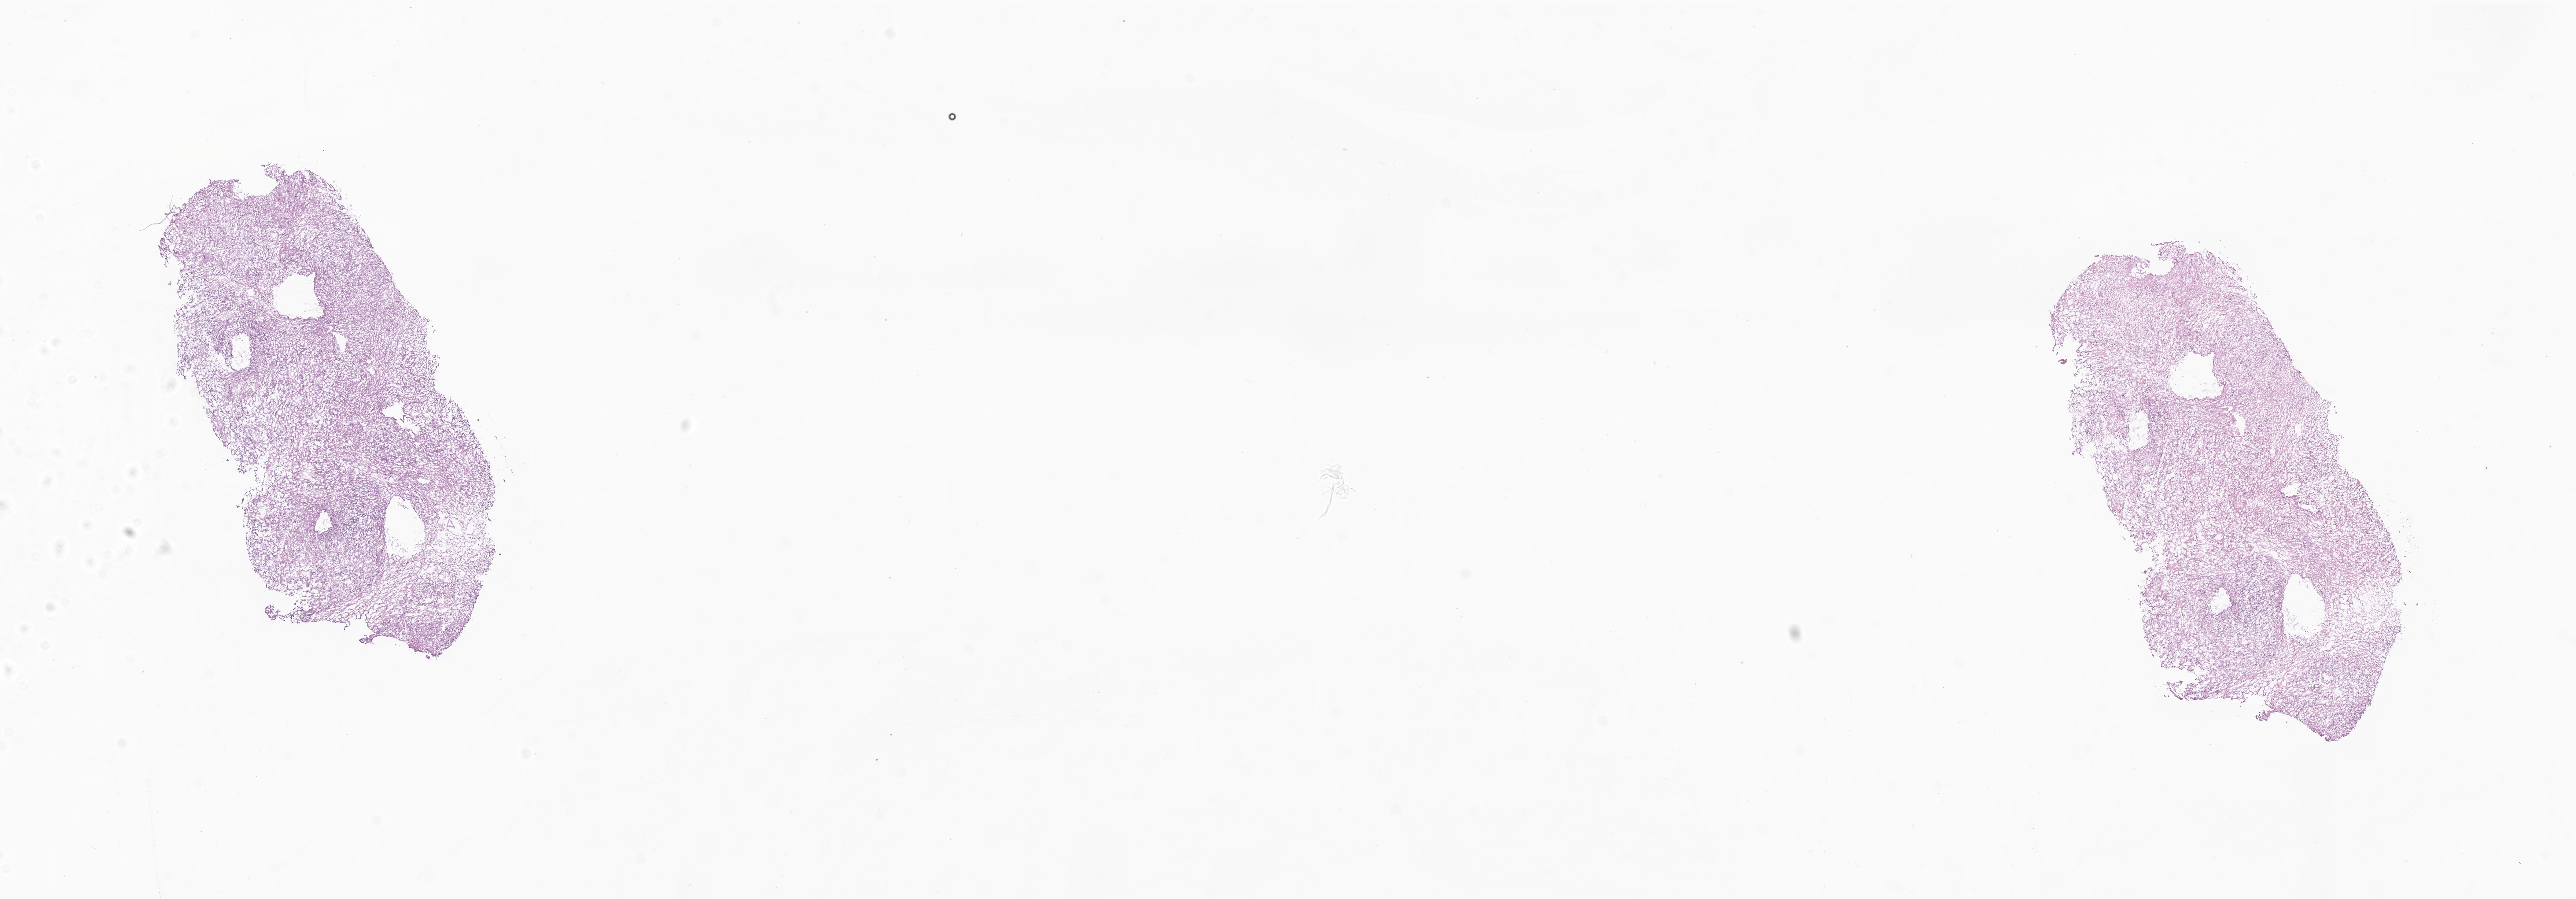
Whole-slide image, H&E stain of tumor tissue from the brain — whole scanned area (about 29.6 x 10.3 mm) shown as a low-resolution overview. Frozen section (OCT-embedded). Male patient, age 110 months (9 years 2 months).
Diagnosis (ICD-O-3 morphology term): Ependymoma, NOS.